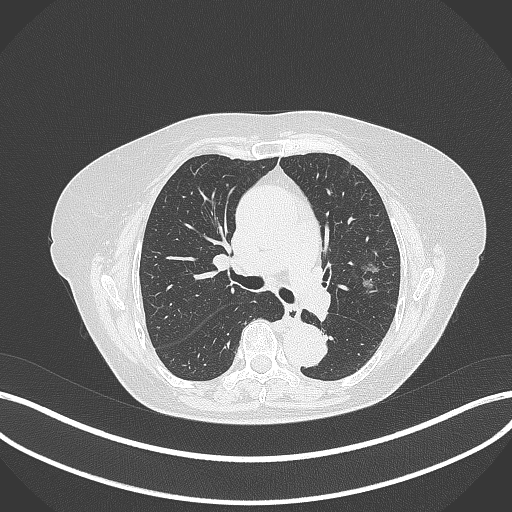
Chest CT, one axial slice; slice 202 of 316 in the series (ordered by position); reconstruction kernel B70f; 120 kVp; lung window (W 1500 / L -600 HU); 1 mm slice thickness; 512 × 512 image matrix, field of view 400 × 400 mm. Patient: female, 75 years. Case-level facts recorded for this patient, not image findings: clinical TNM (as recorded): T1c N0 M0.
Annotated regions visible in this slice (rectangle marked by the reading radiologist):
- lung tumour (recorded histology: adenocarcinoma): bounding box [x1, y1, x2, y2] px = [358, 264, 380, 294]